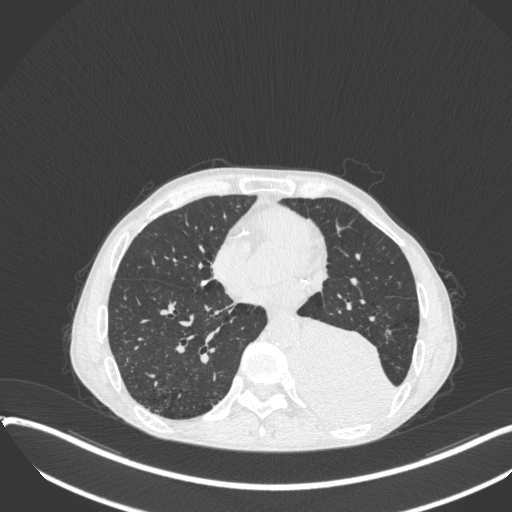
Chest CT, one axial slice. Slice 139 of 400 in the series (ordered by position). 120 kVp. Lung window (W 1500 / L -600 HU). 512 × 512 image matrix. Patient: male, 57 years. From the clinical record (not read from this slice): clinical TNM (as recorded): T4 N0 M0.
Outlined on this slice (rectangle marked by the reading radiologist):
- lung tumour (recorded histology: squamous cell carcinoma): bounding box <294,317,404,422> (left, top, right, bottom; pixels)